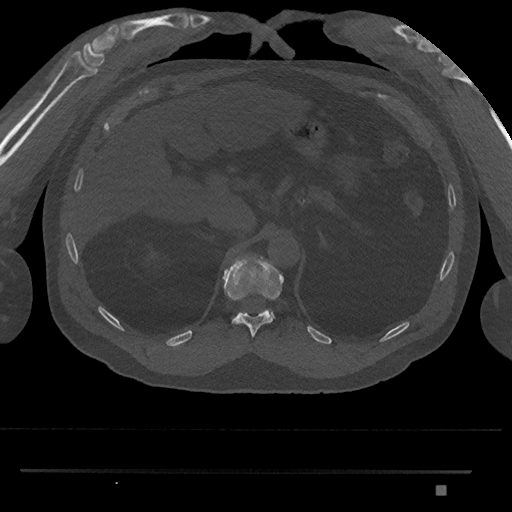
CT including the spine, one axial slice. Position 935 of 1134 along the scan axis. Bone window (W 1800 / L 400 HU). 0.5 mm slice thickness. 512 × 512 image matrix, field of view 429 × 429 mm. Male patient, age 65 years. Case-level facts recorded for this patient, not image findings: primary cancer: prostate.
Structures marked on this image (semi-automatically segmented with operator editing):
- T11 vertebra: box from (x=222, y=257) to (x=284, y=338) px
- T12 vertebra: (x=237, y=311)–(x=276, y=318)